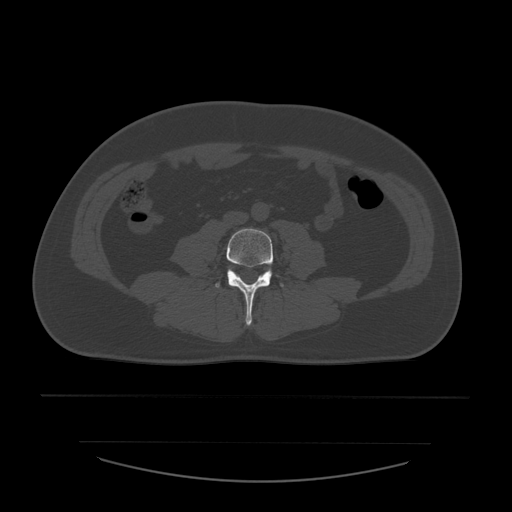
CT including the spine, one axial slice; slice 146 of 532 in the series (ordered by position); reconstruction kernel STANDARD; 120 kVp; bone window (W 1800 / L 400 HU); 1.25 mm slice thickness; 512 × 512 image matrix, field of view 441 × 441 mm. Patient age 44 years. Case-level facts recorded for this patient, not image findings: primary cancer: soft tissue sarcoma.
Annotated regions visible in this slice (semi-automatic segmentation, software-assisted and operator-edited):
- L4 vertebra: bounding box (x1, y1, x2, y2) in pixels: (215, 229, 284, 326)